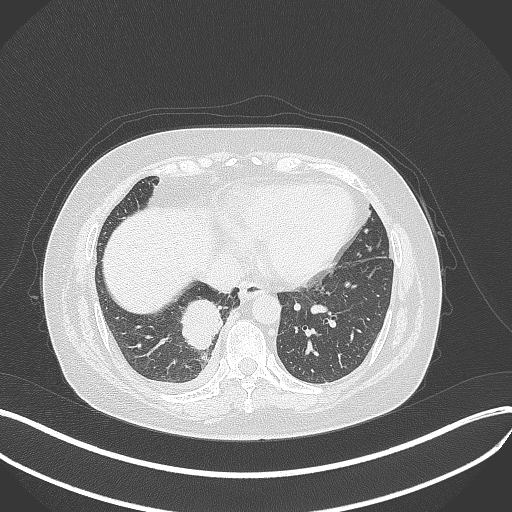
Chest CT, one axial slice; position 110 of 381 along the scan axis; reconstruction kernel B70f; lung window (W 1500 / L -600 HU); 512 × 512 image matrix. Patient: female, 56 years. Case-level facts recorded for this patient, not image findings: clinical TNM (as recorded): T2b N1 M0.
Outlined on this slice (rectangle marked by the reading radiologist):
- lung tumour (recorded histology: small cell carcinoma): bounding box <182,296,225,351> (left, top, right, bottom; pixels)